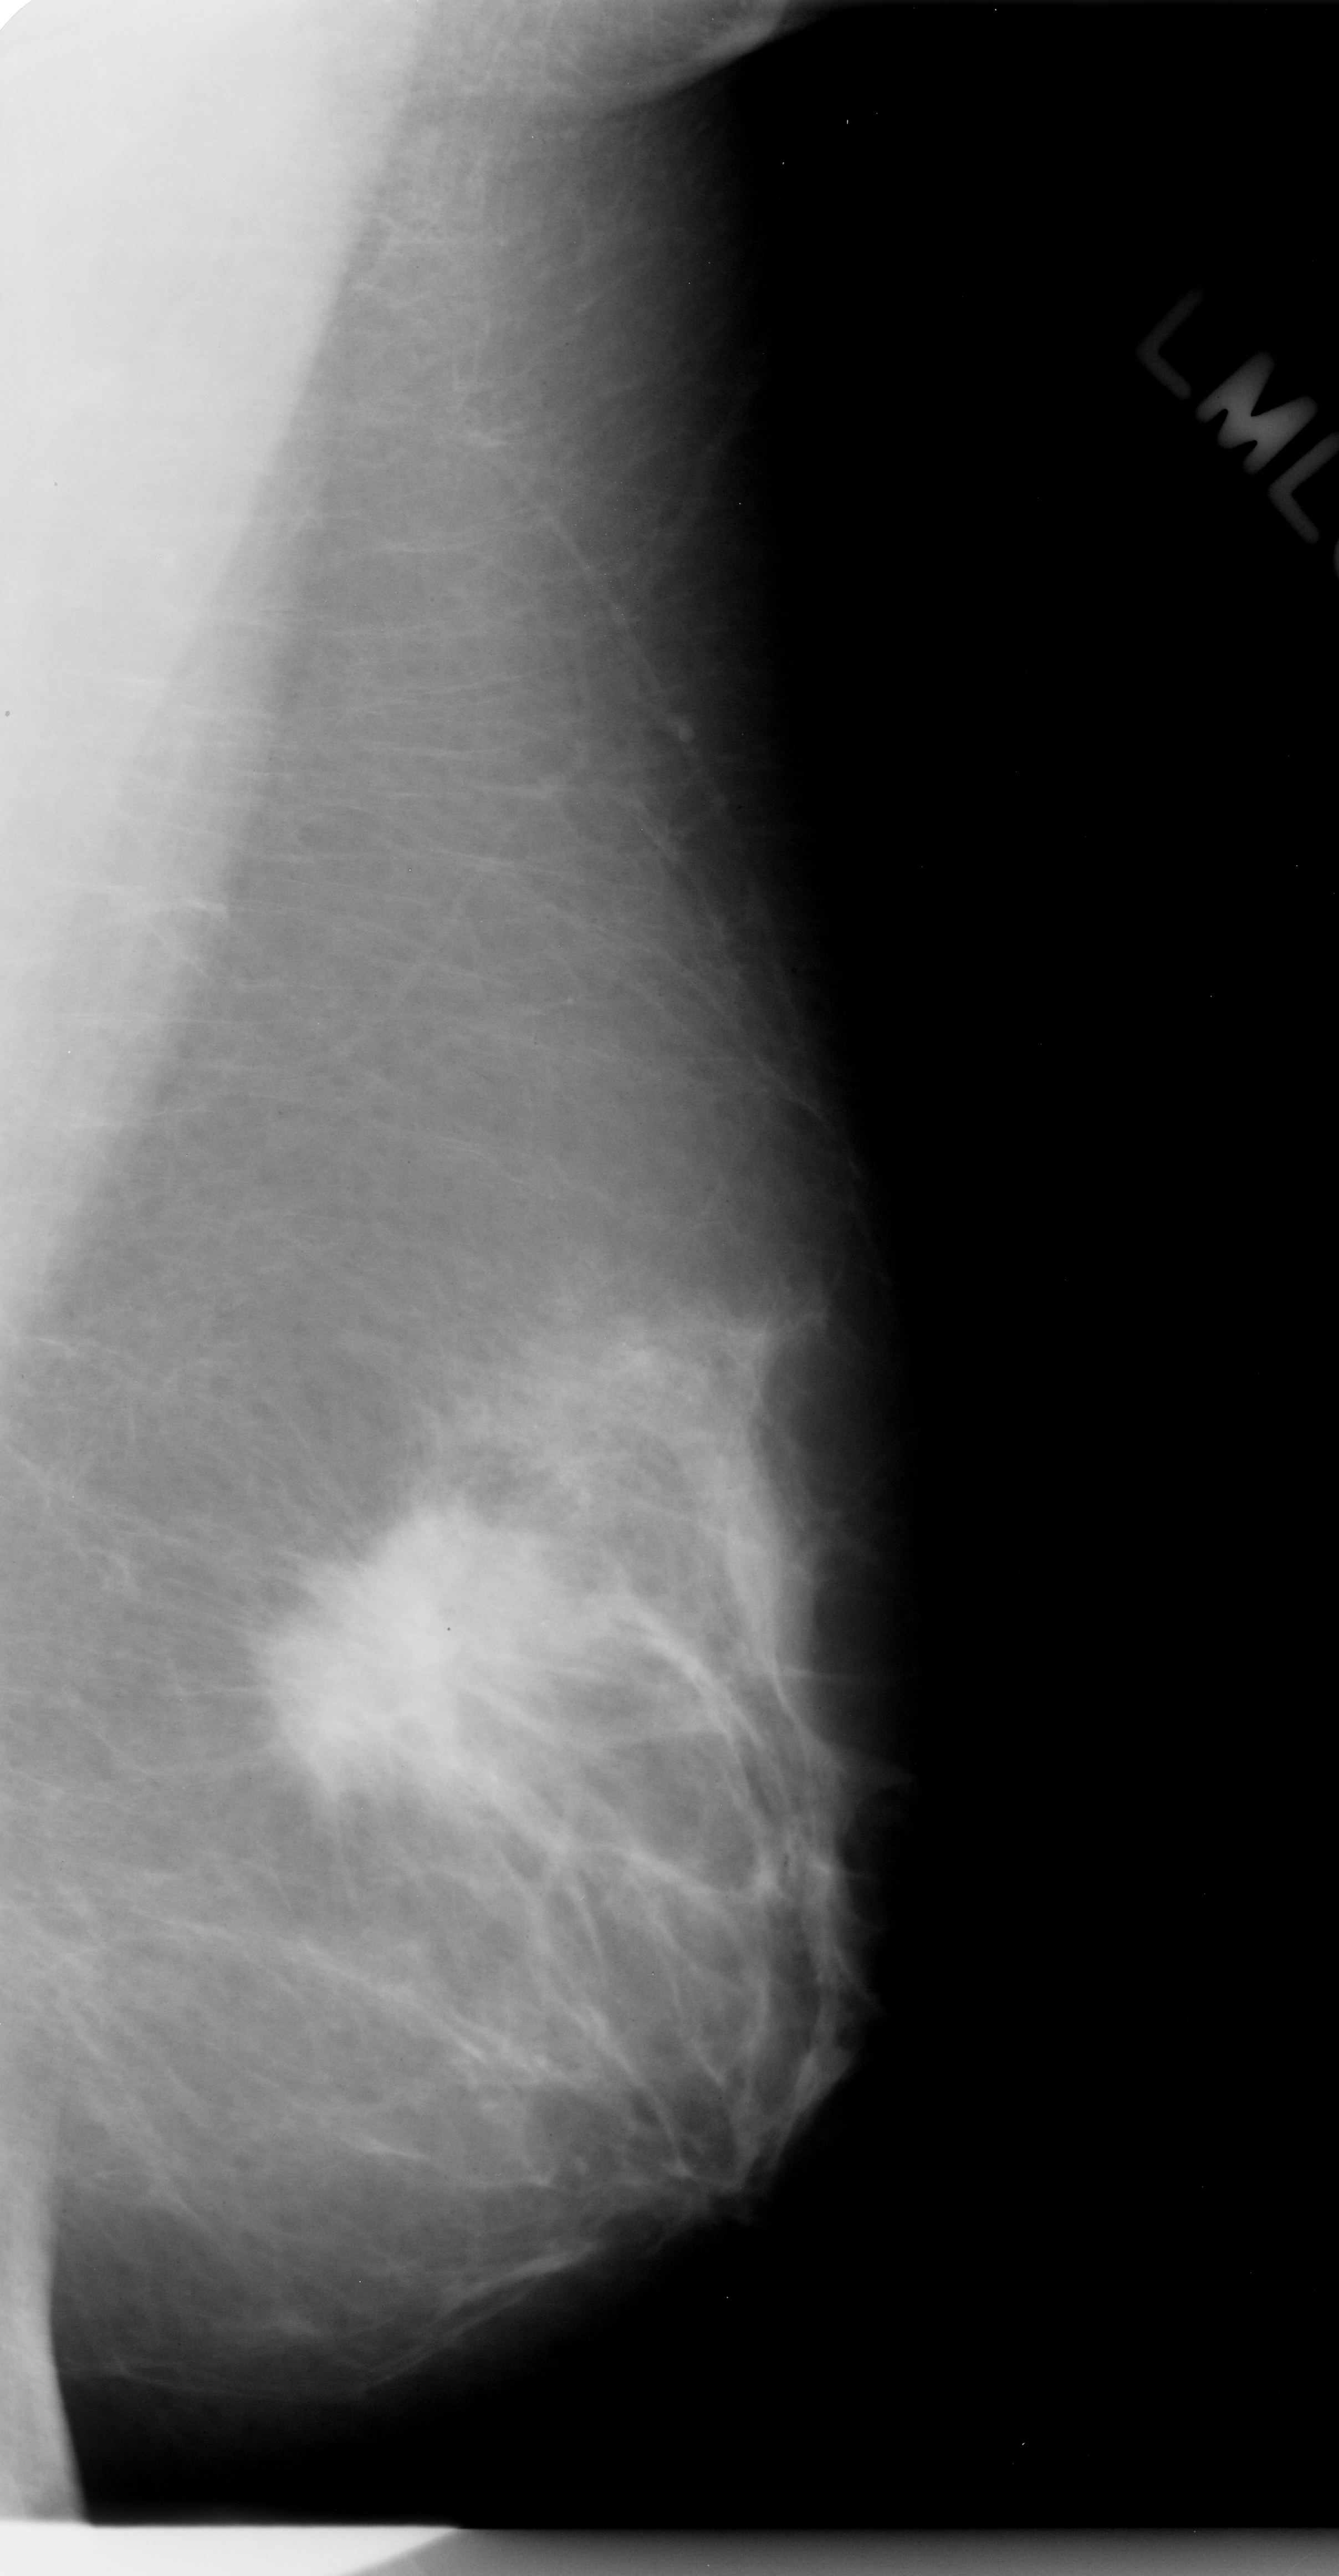
Digitized screen-film mammogram. Left breast. Mediolateral oblique (MLO) view. BI-RADS breast density category 2 (scale 1–4). 1339 × 2576 image matrix.
Marked abnormalities (boxes around the expert regions of interest):
- mass, shape irregular, margins spiculated; BI-RADS assessment category 5; subtlety rating 5 on a 1 (subtle) to 5 (obvious) scale; pathology result (as recorded, not read from the image): malignant: bounding box [x1, y1, x2, y2] px = [264, 1504, 560, 1782]